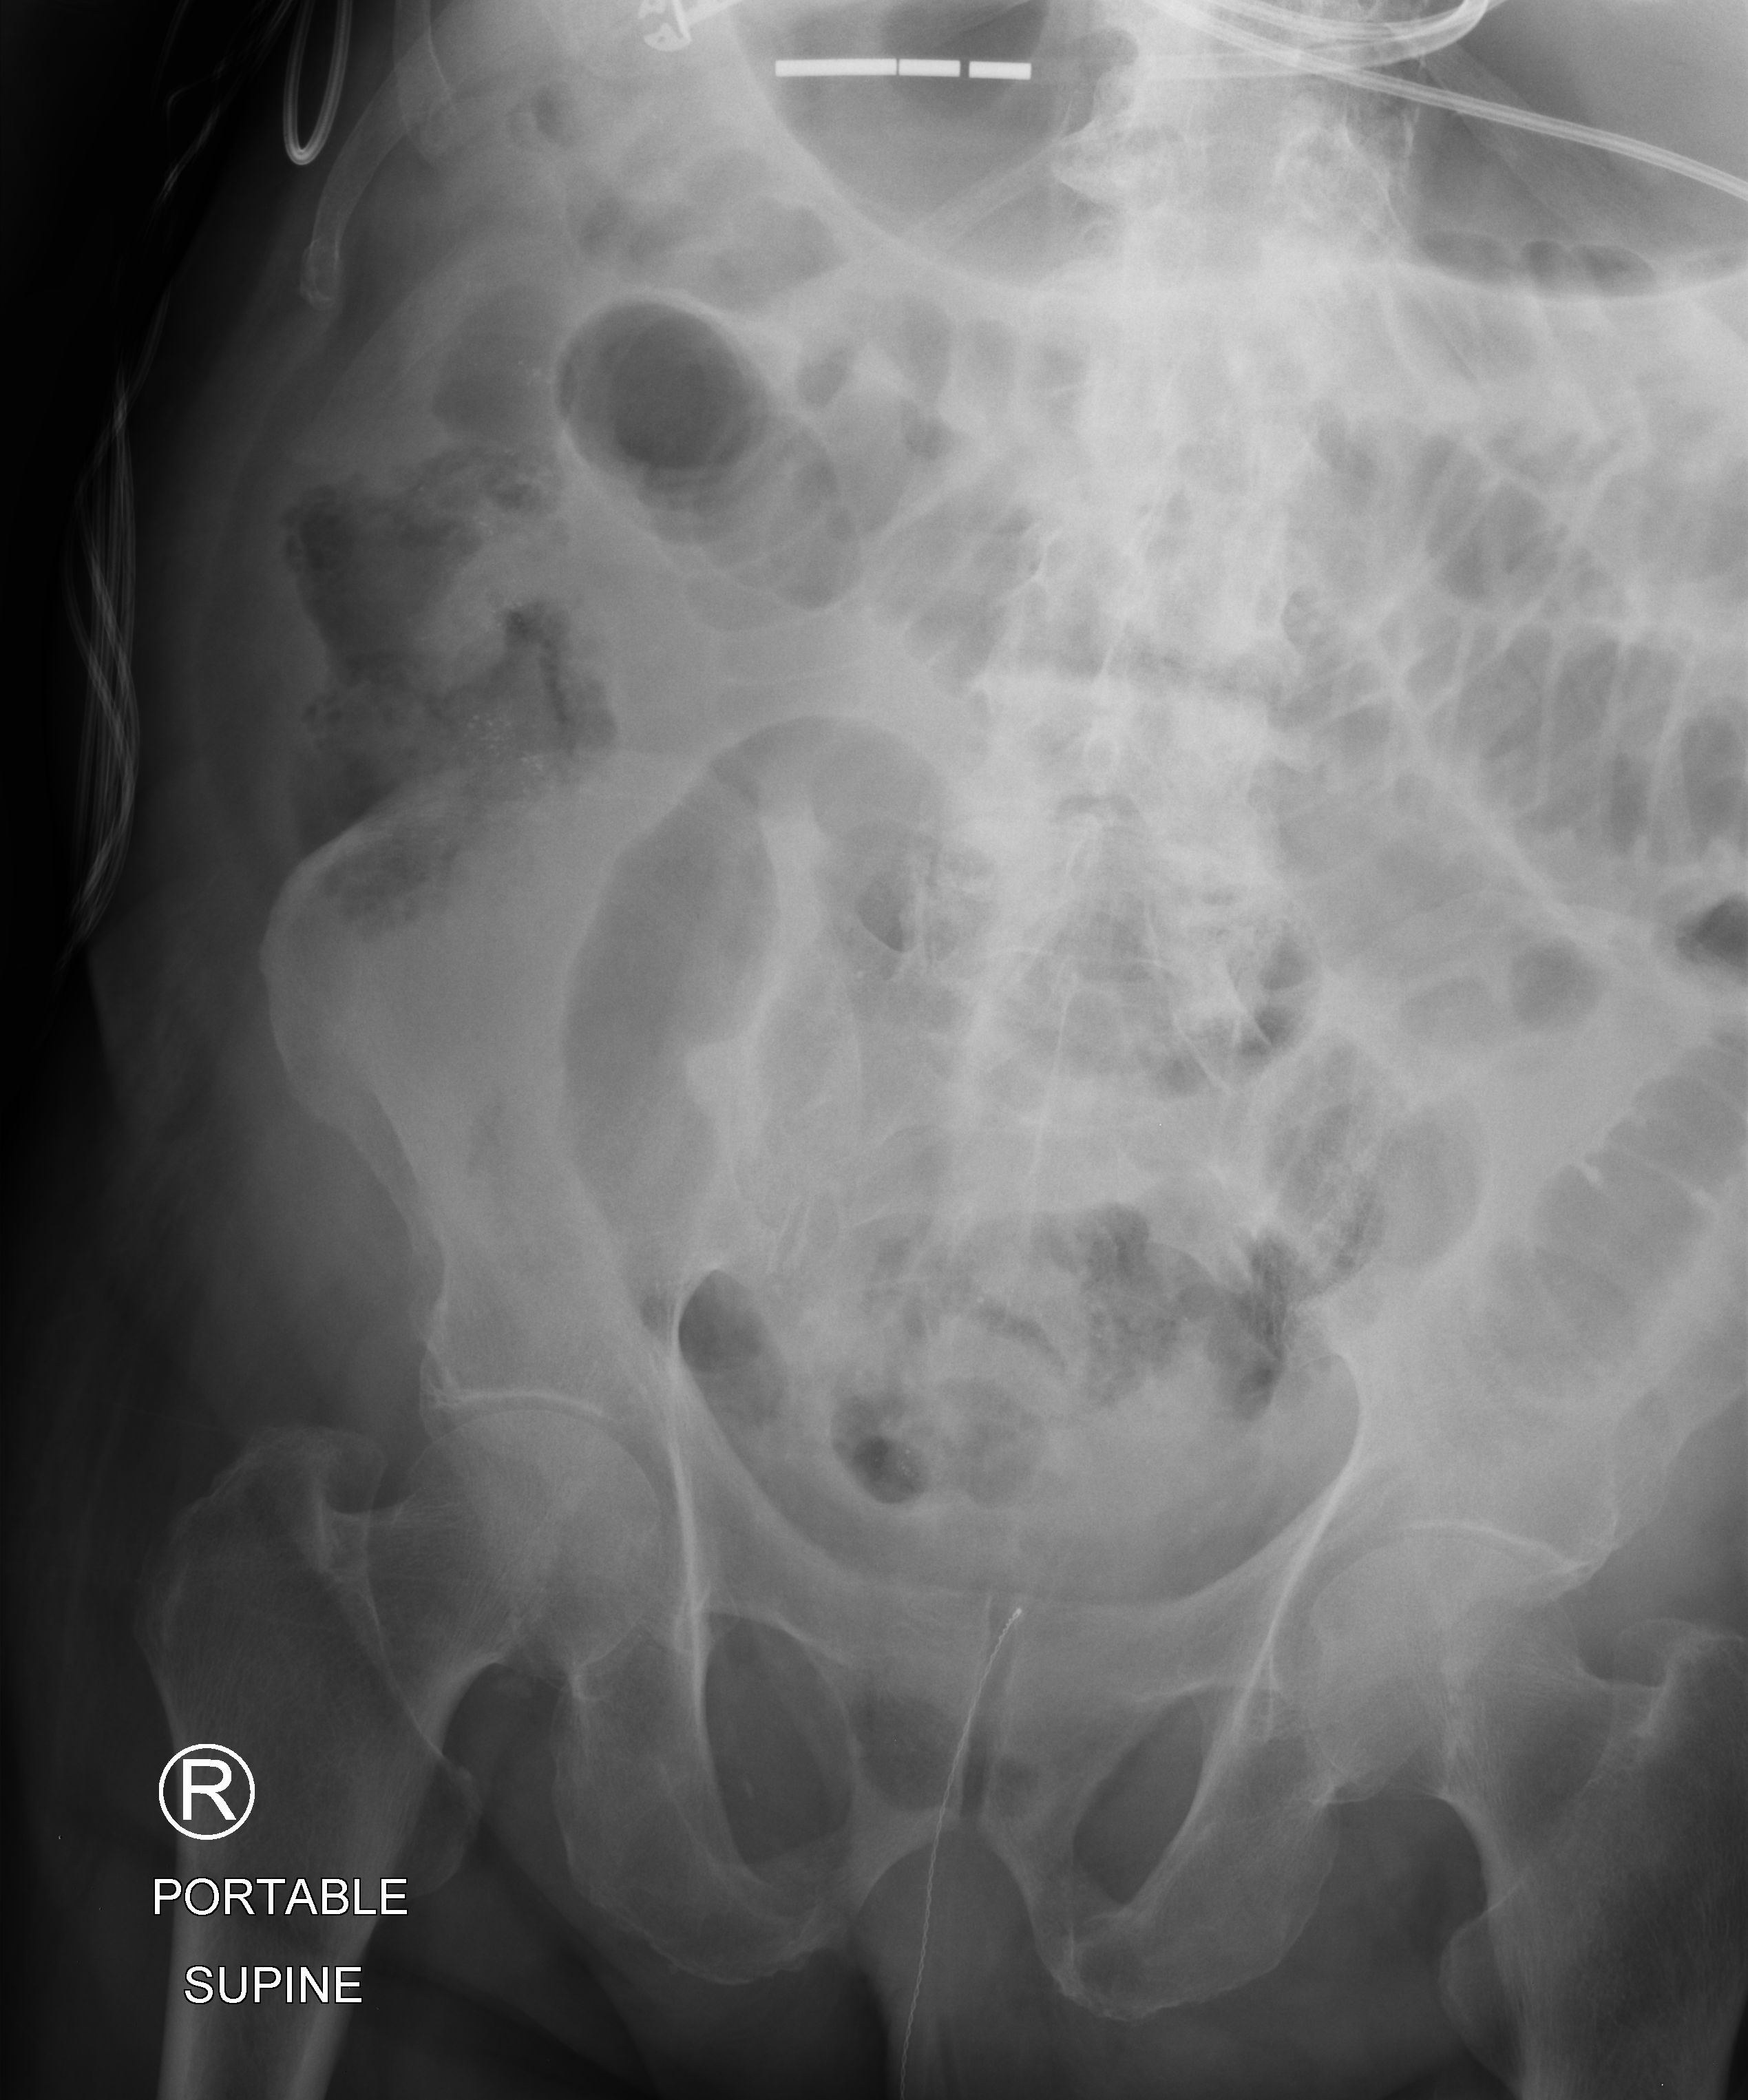
Bedside abdomen radiograph (computed radiography); anteroposterior (AP) projection. Male patient hospitalised with COVID-19, age 75–90 years.
Admission-level facts for this patient (not findings on this image; timing relative to this image not recorded):
- smoking status (admission record): former